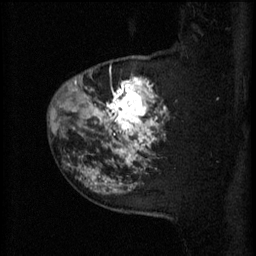
Breast MRI (dynamic contrast-enhanced), one sagittal slice; 3 images stored at this slice position (order not interpretable as contrast timing); 1.5 T; TE 4.2 ms, TR 11 ms; 2 mm slice thickness; 256 × 256 image matrix. Female patient, age 52 years.
Outlined on this slice (semi-automatic segmentation, software-assisted and operator-edited):
- analysis volume of interest (the breast-tissue region the enhancement analysis was run in; not a lesion): bounding box <81,56,169,157> (left, top, right, bottom; pixels)
- tumour enhancement mask (voxels above the 70 % enhancement threshold inside the analysis volume of interest): <81,70,167,157>